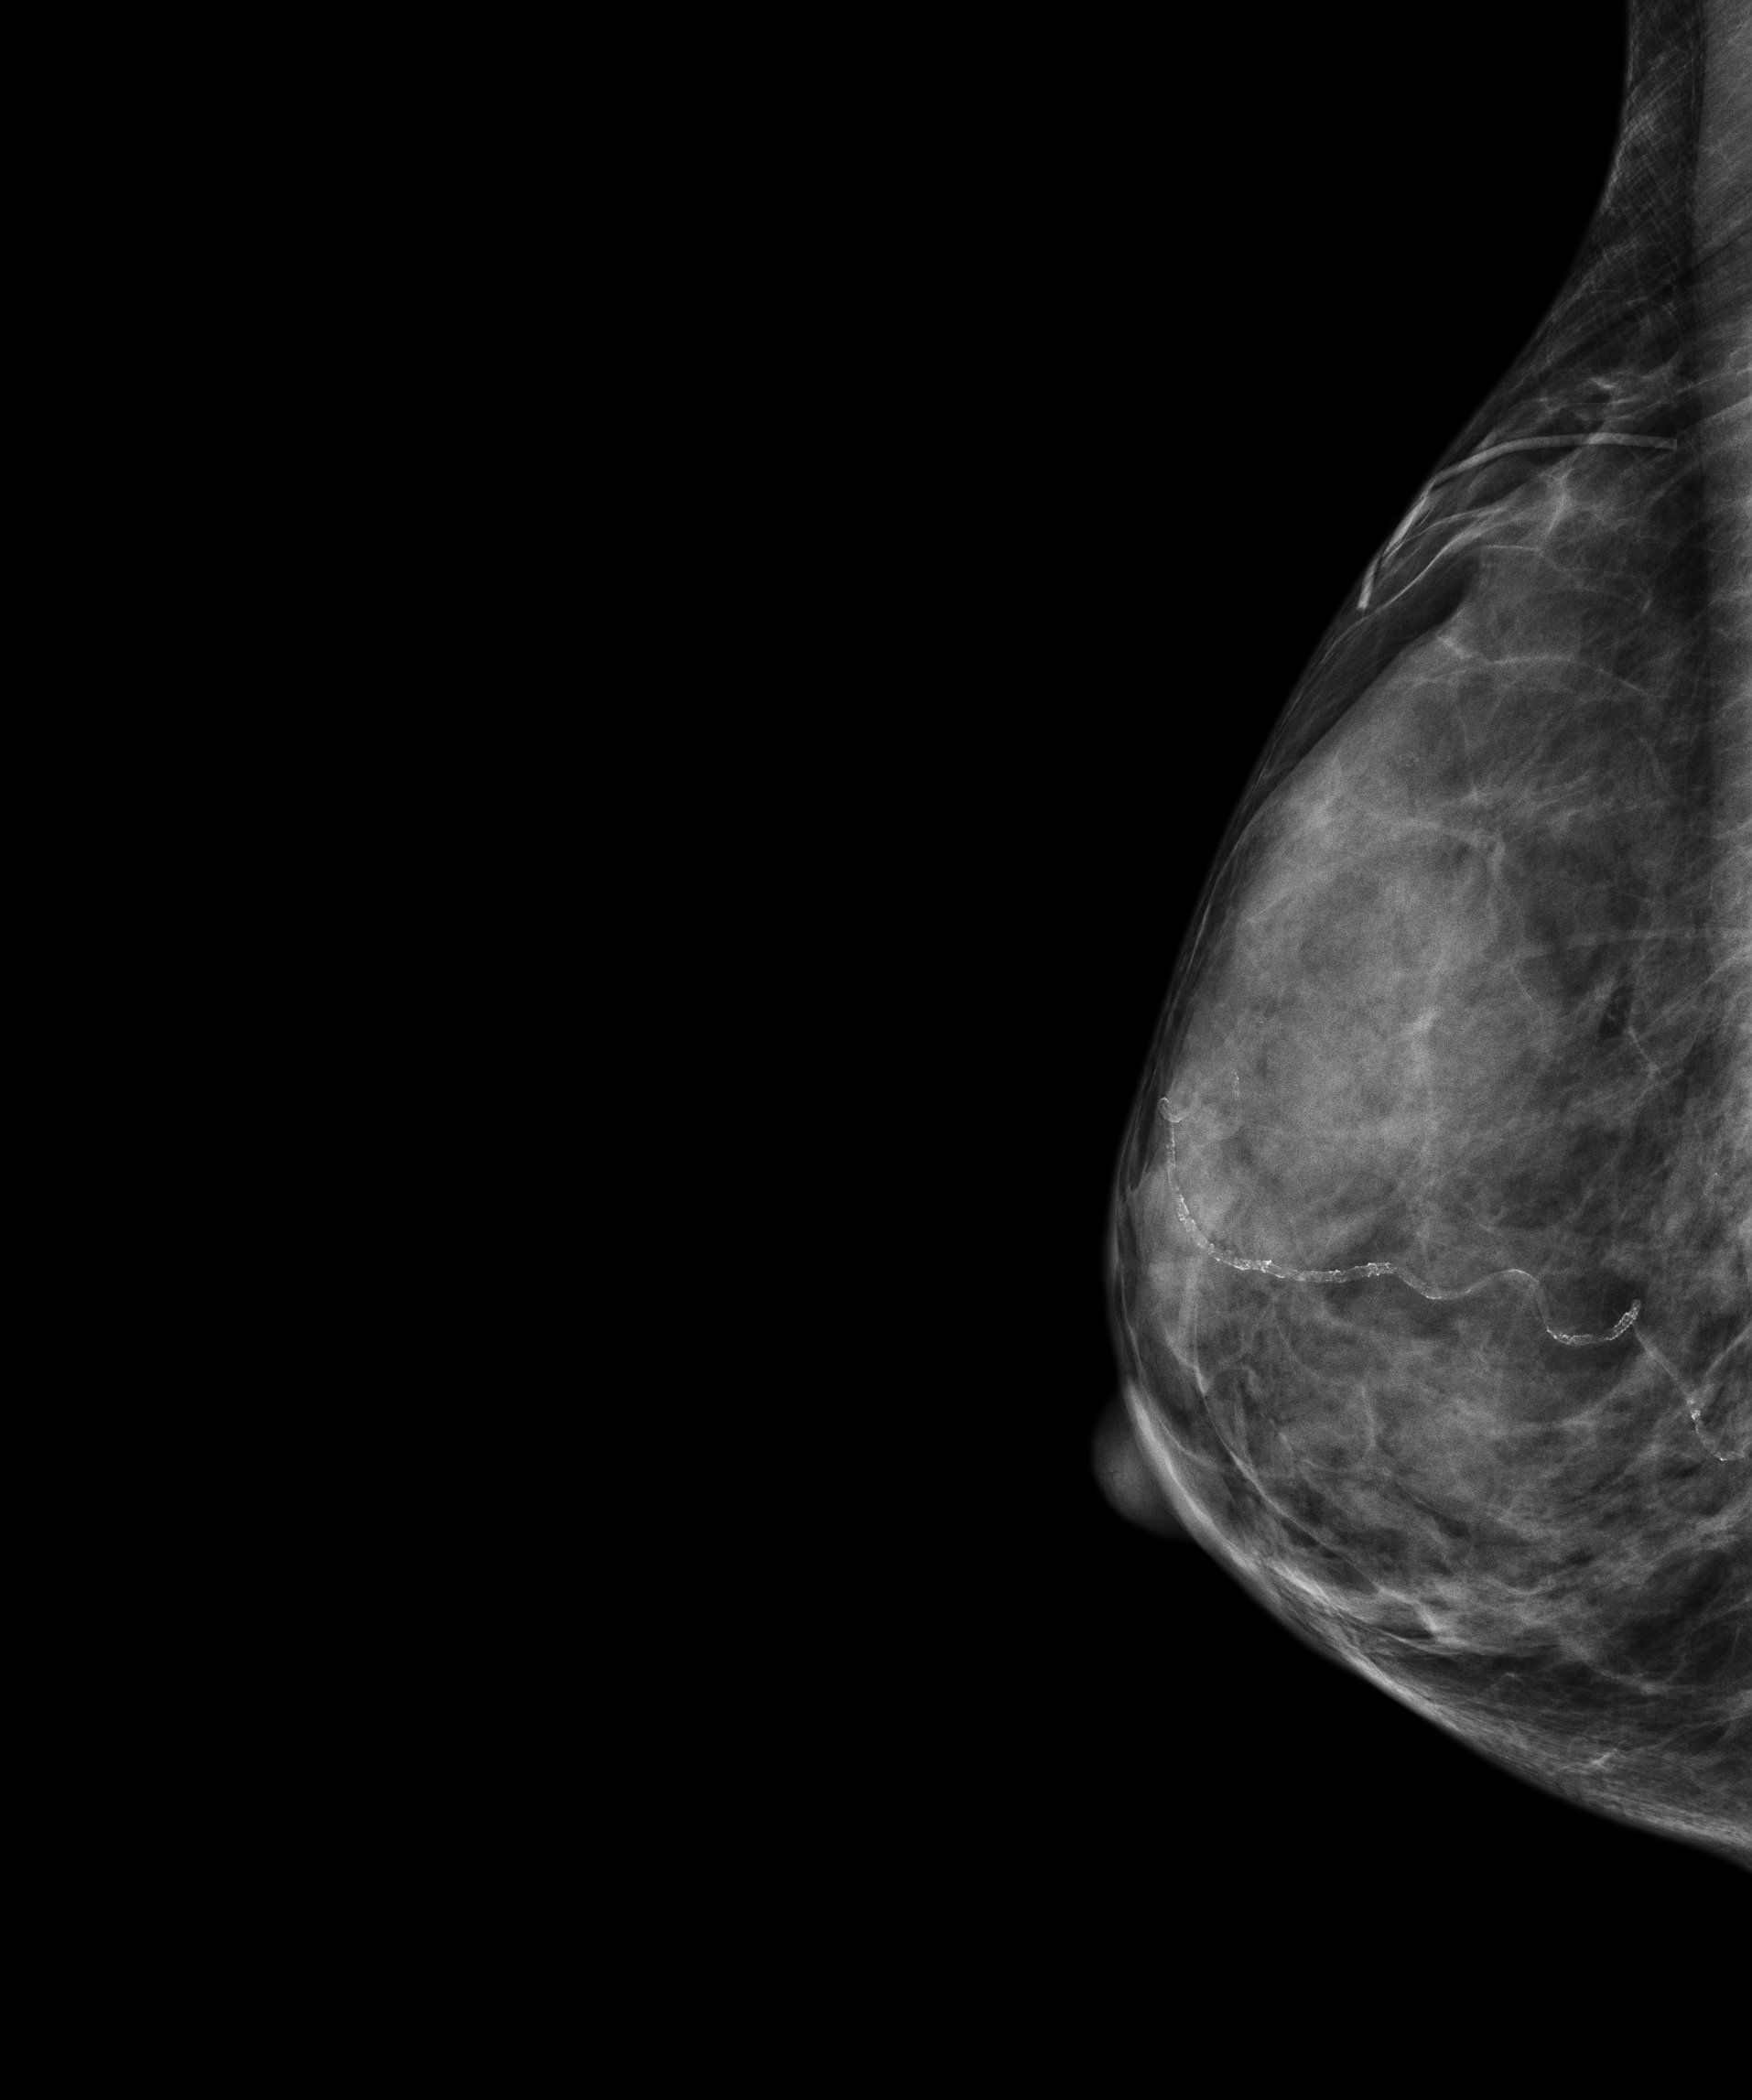
Digital mammogram (FFDM); right breast; laterally exaggerated craniocaudal (XCCL) view; annual screening mammography examination; compressed breast thickness 28 mm. Patient aged 59 years (female).
- breast density at the screening exam (both breasts): extremely dense (BI-RADS density category d)
- final BI-RADS category for the screening round (tomosynthesis exam, both breasts): category 1
- recall: no recall after this screen